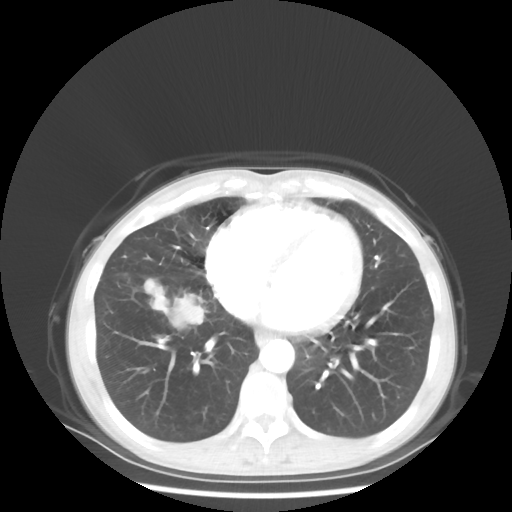
Chest CT, one axial slice. Slice 20 of 56 in the series (ordered by position). Reconstruction kernel STANDARD. Lung window (W 1500 / L -600 HU). 512 × 512 image matrix. Patient: female, 57 years. From the clinical record (not read from this slice): clinical TNM (as recorded): T1c N3 M1a; histopathological grade: G3.
Annotated regions visible in this slice (rectangle marked by the reading radiologist):
- lung tumour (recorded histology: adenocarcinoma): box from (x=142, y=282) to (x=207, y=331) px